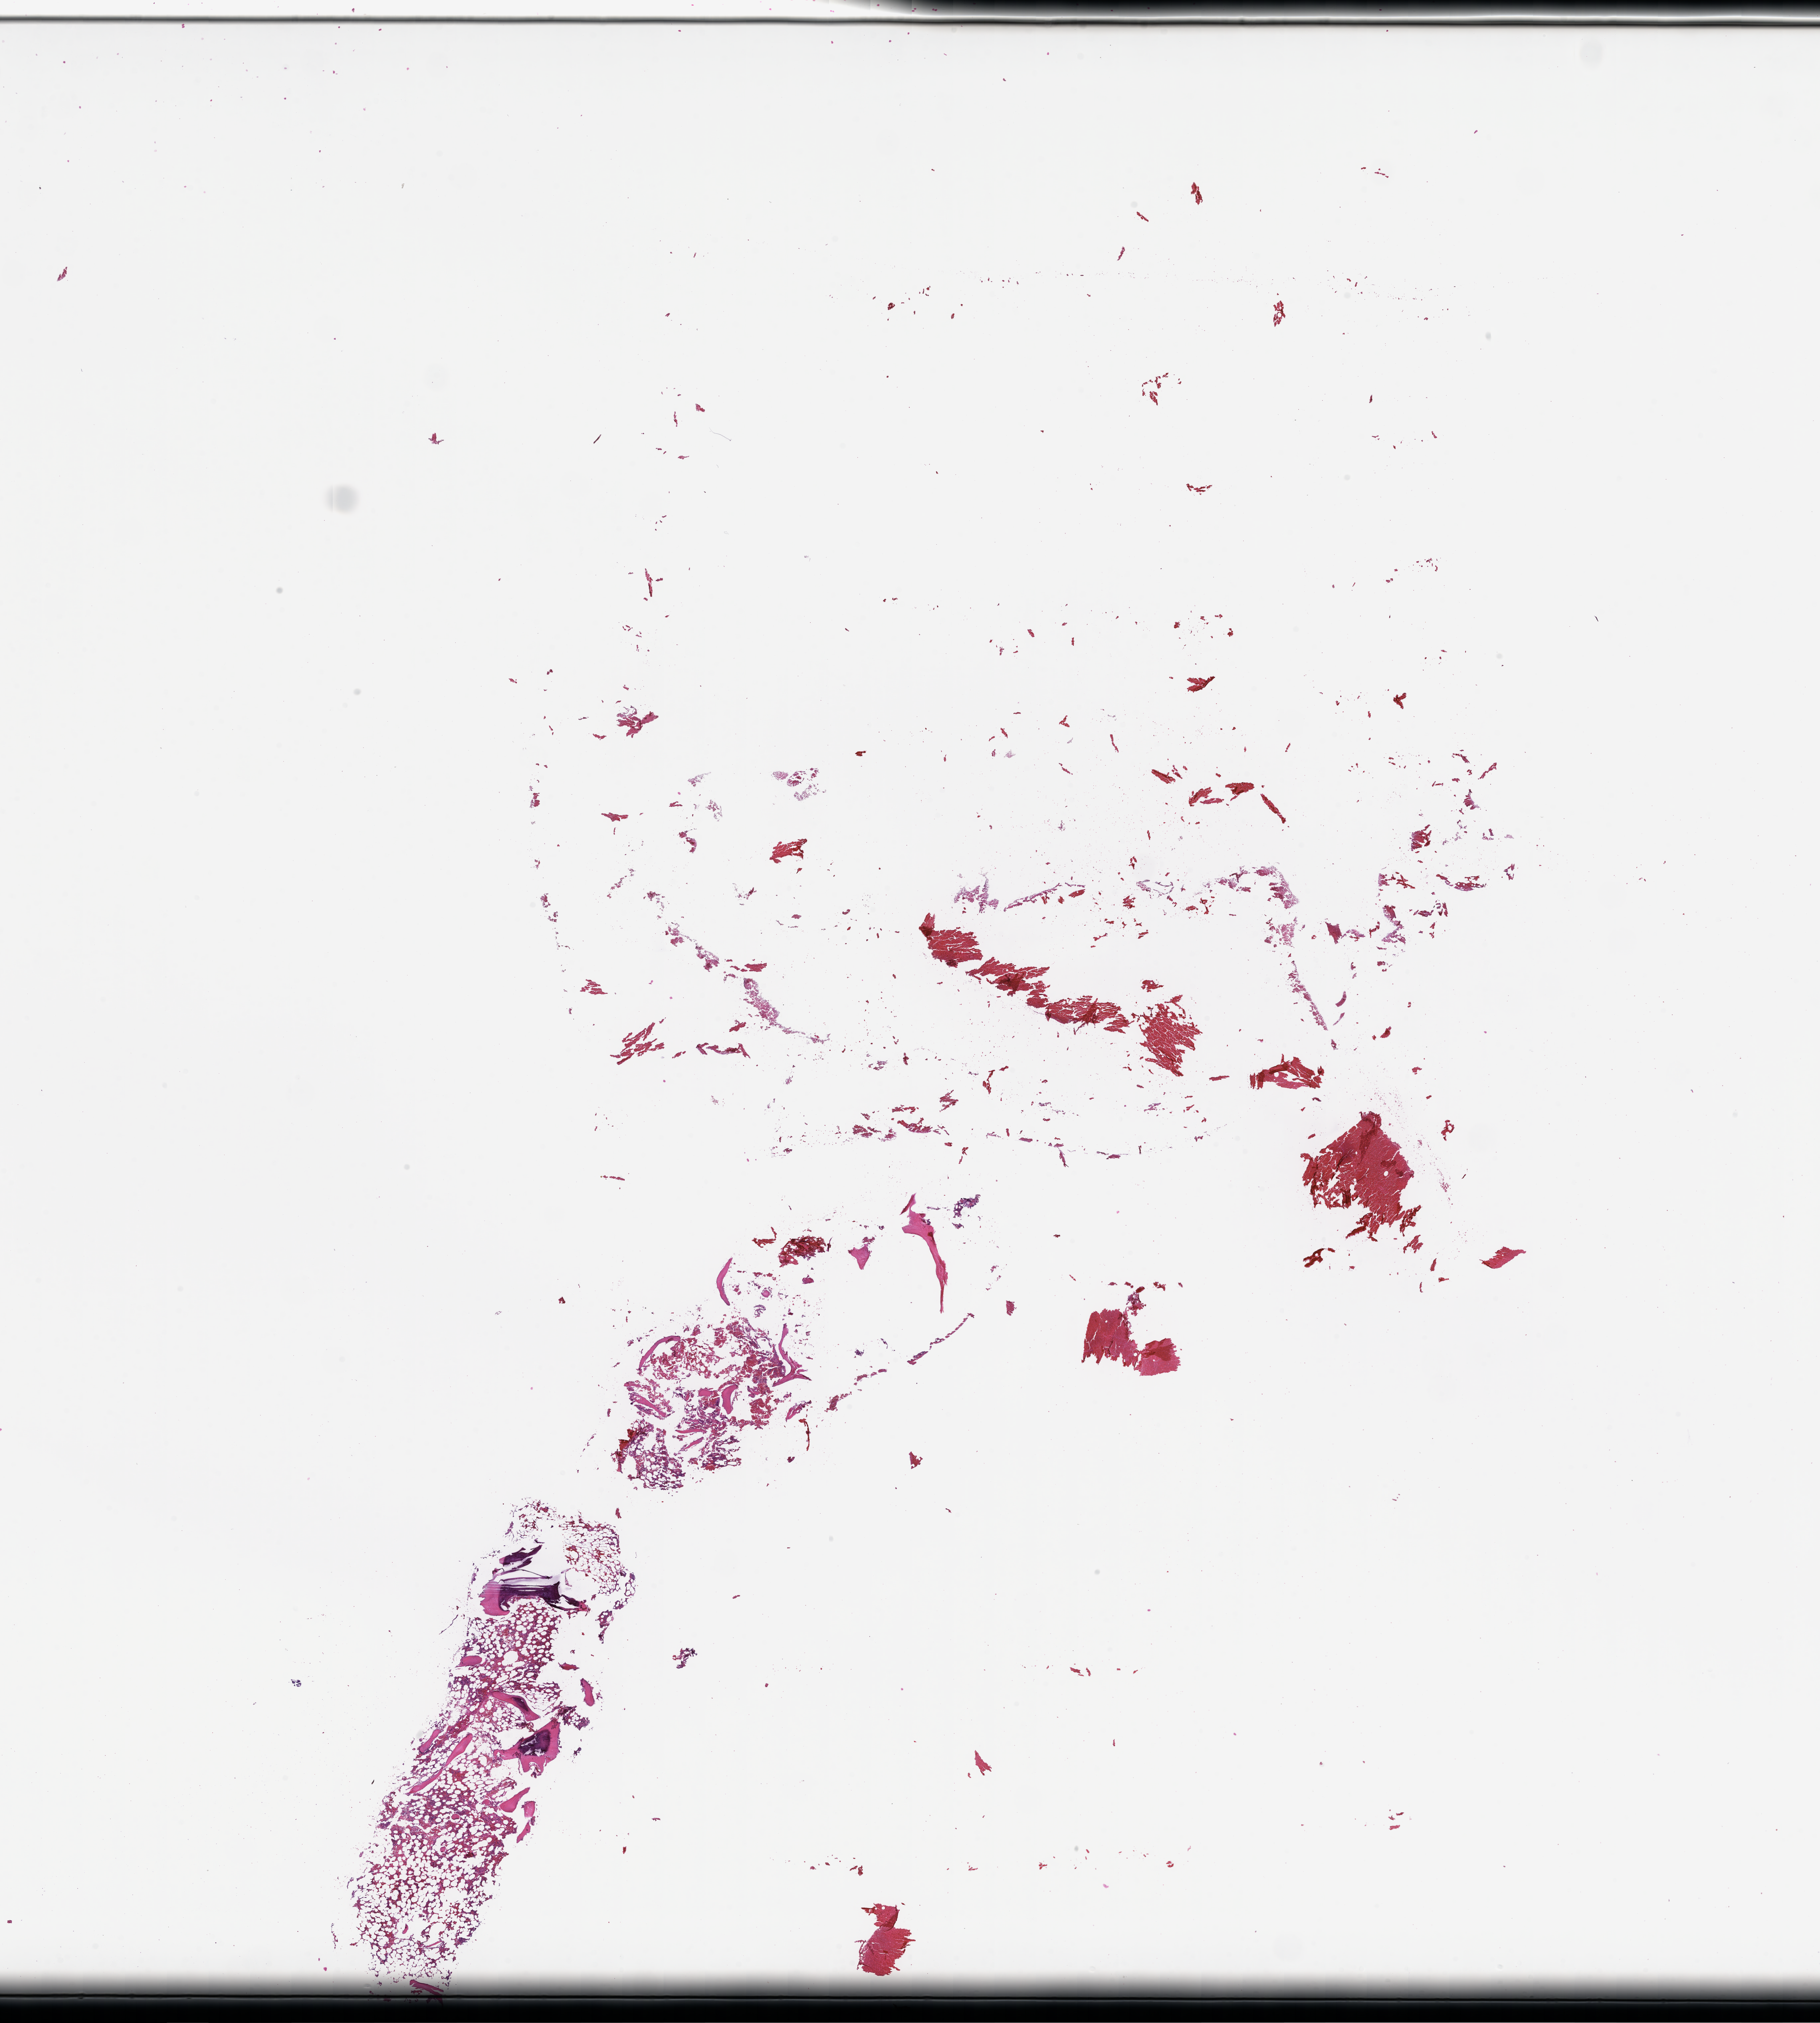
H&E whole-slide image — shown as a low-resolution overview of the whole scanned area (about 22.1 x 24.6 mm). Formalin-fixed paraffin-embedded section. Site: bone marrow. Patient: male.
This section: primary tumour tissue. Diagnosis: Plasma Cell Myeloma.